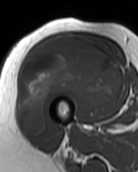
MRI of an extremity soft-tissue mass, one axial slice; MR volume resampled by the dataset authors to the PET/CT grid (not the native acquisition matrix); 3.27 mm slice thickness; 138 × 172 image matrix. Female patient. Case-level facts recorded for this patient, not image findings: histological type: pleiomorphic undifferentiated sarcoma; grade: high; site of the primary tumour: right quadricep.
Annotated regions visible in this slice (expert contour drawn on MRI and transferred to this co-registered scan by the dataset authors):
- gross tumour volume including surrounding oedema: bounding box <19,34,122,135> (left, top, right, bottom; pixels)
- gross tumour volume (mass): <19,34,122,135>